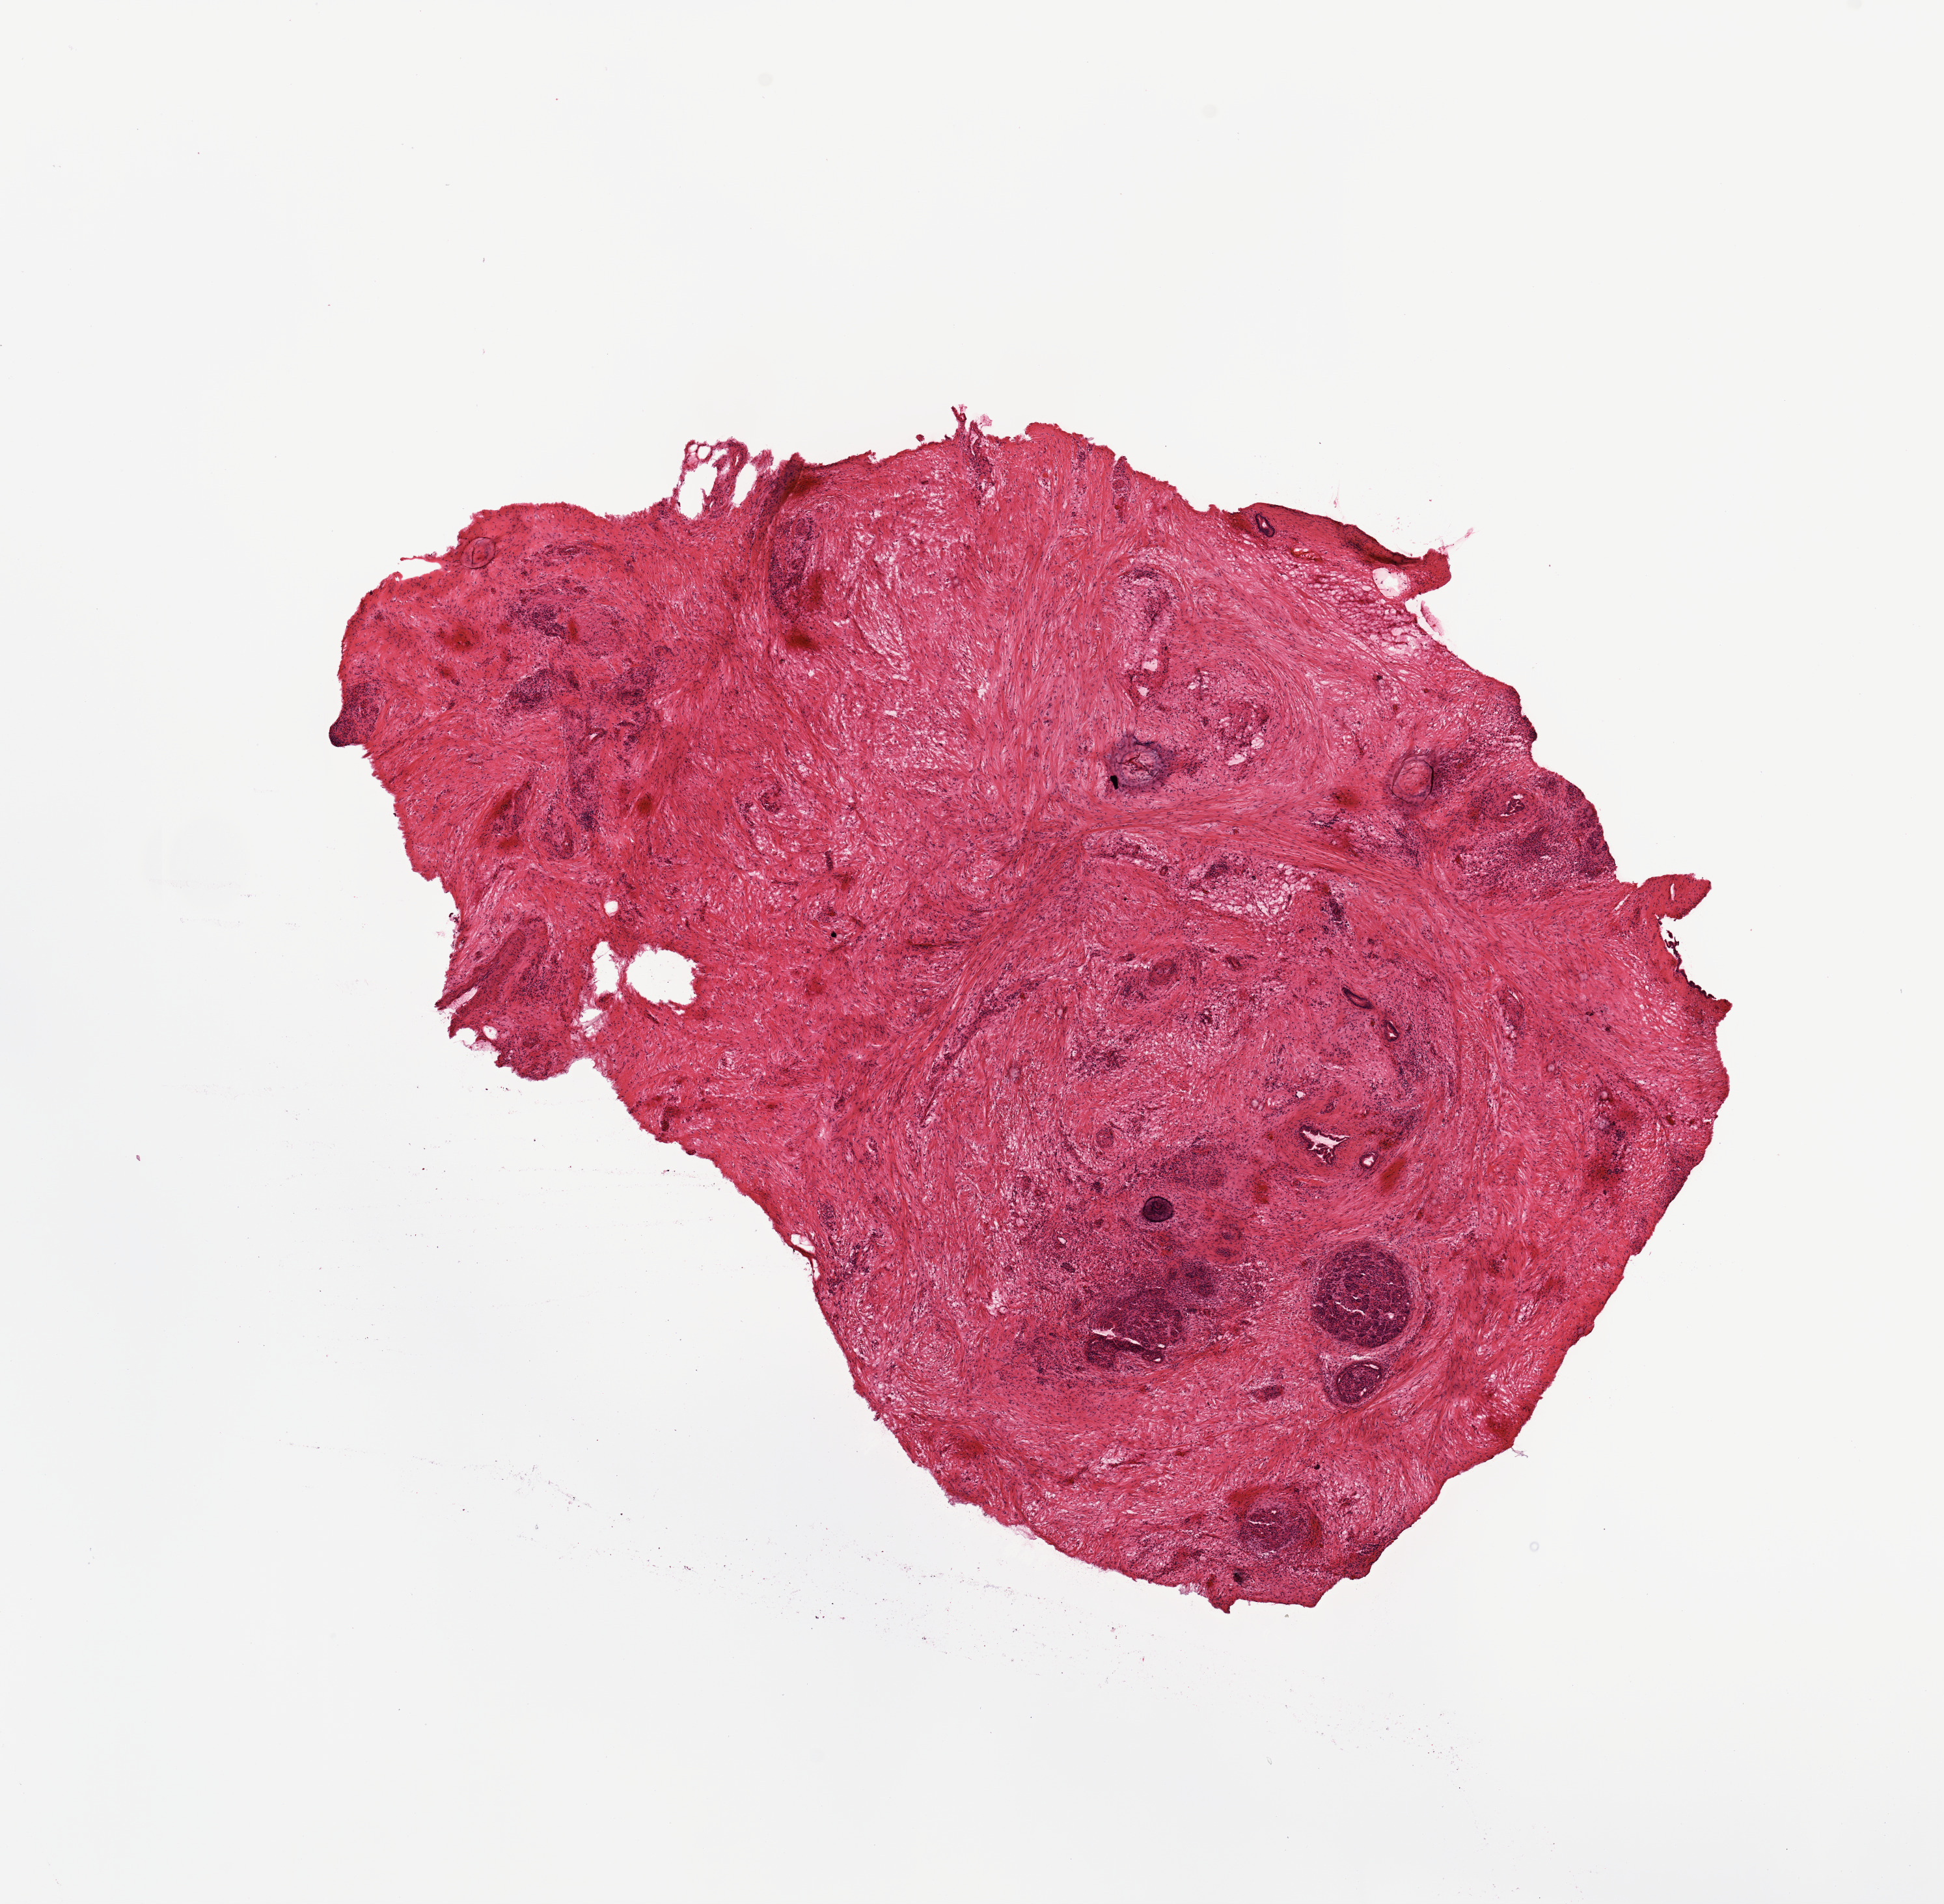
Digitized H&E tissue section (whole slide) — whole scanned area (about 11.8 x 11.6 mm) shown as a low-resolution overview; pancreas, normal (non-tumour) tissue. Female, 61 y/o.
This section: normal (non-tumour) tissue from the same patient. Patient diagnosis: Infiltrating duct carcinoma, NOS.